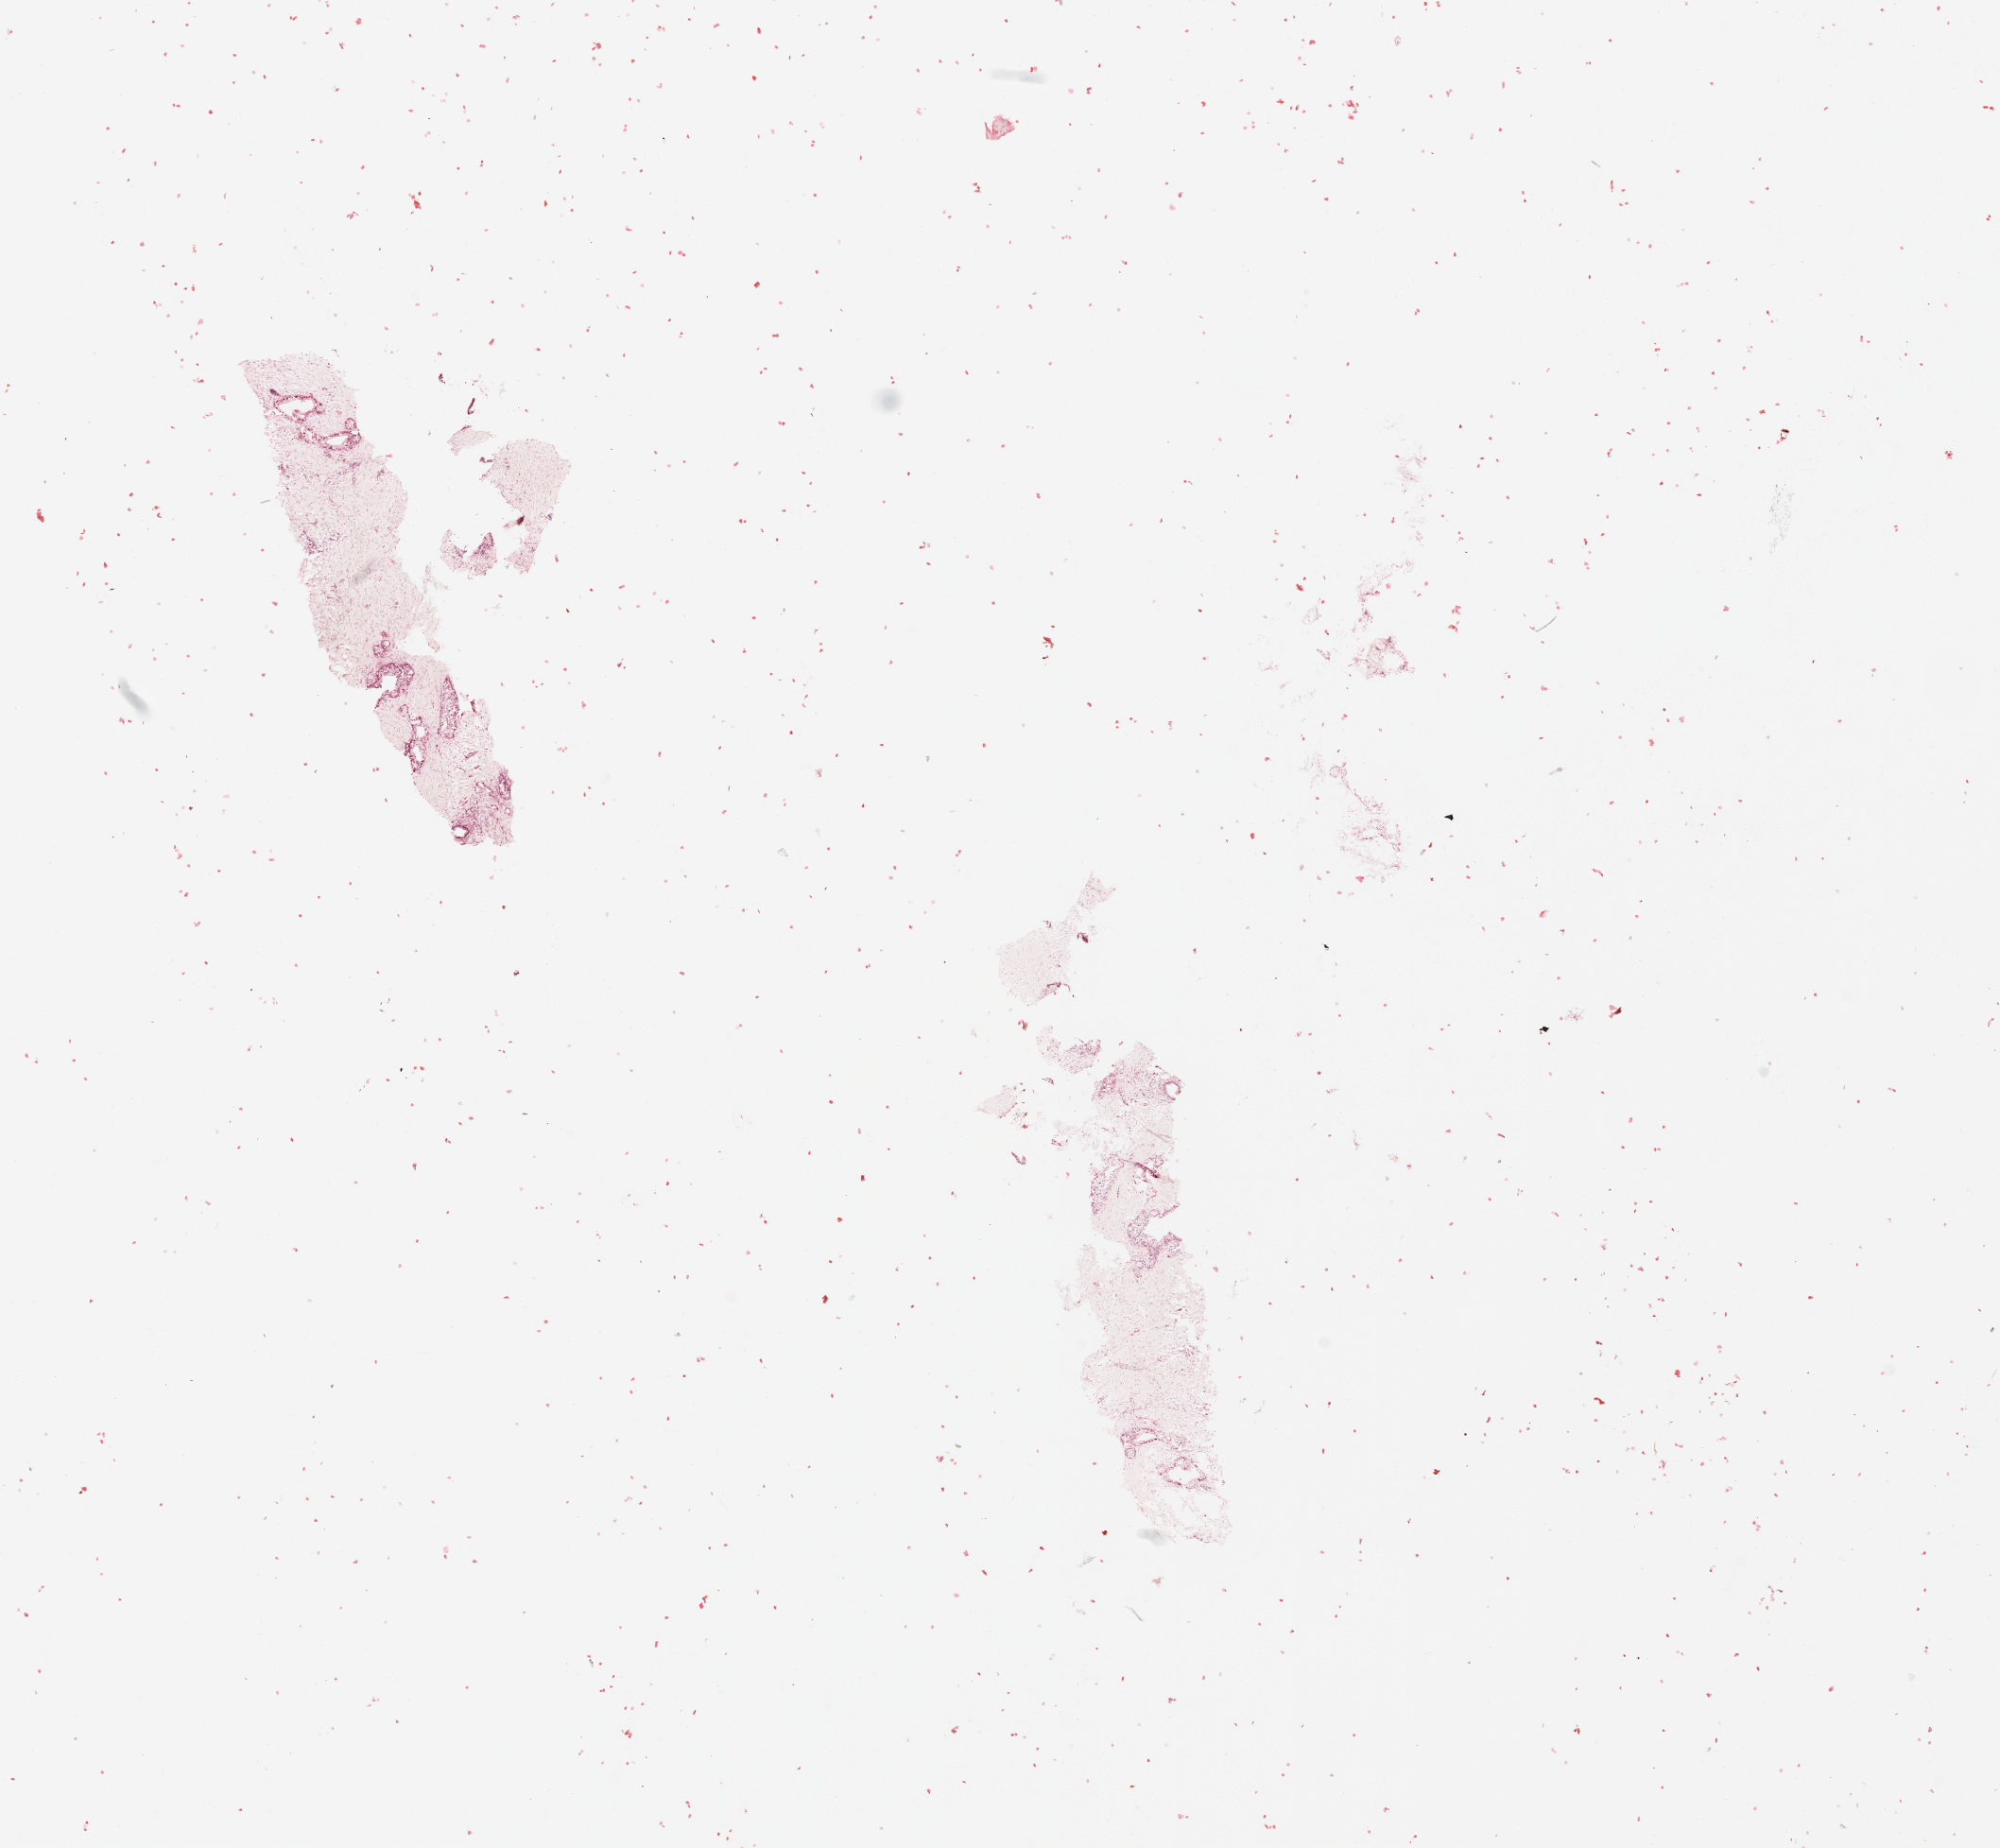
Whole-slide histology image, H&E-stained — a low-resolution overview of the entire scanned area, about 16.7 x 15.5 mm (from a 20x scan); pancreas, tumour tissue. Patient: male, age 56 years.
Diagnosis: Infiltrating duct carcinoma, NOS.